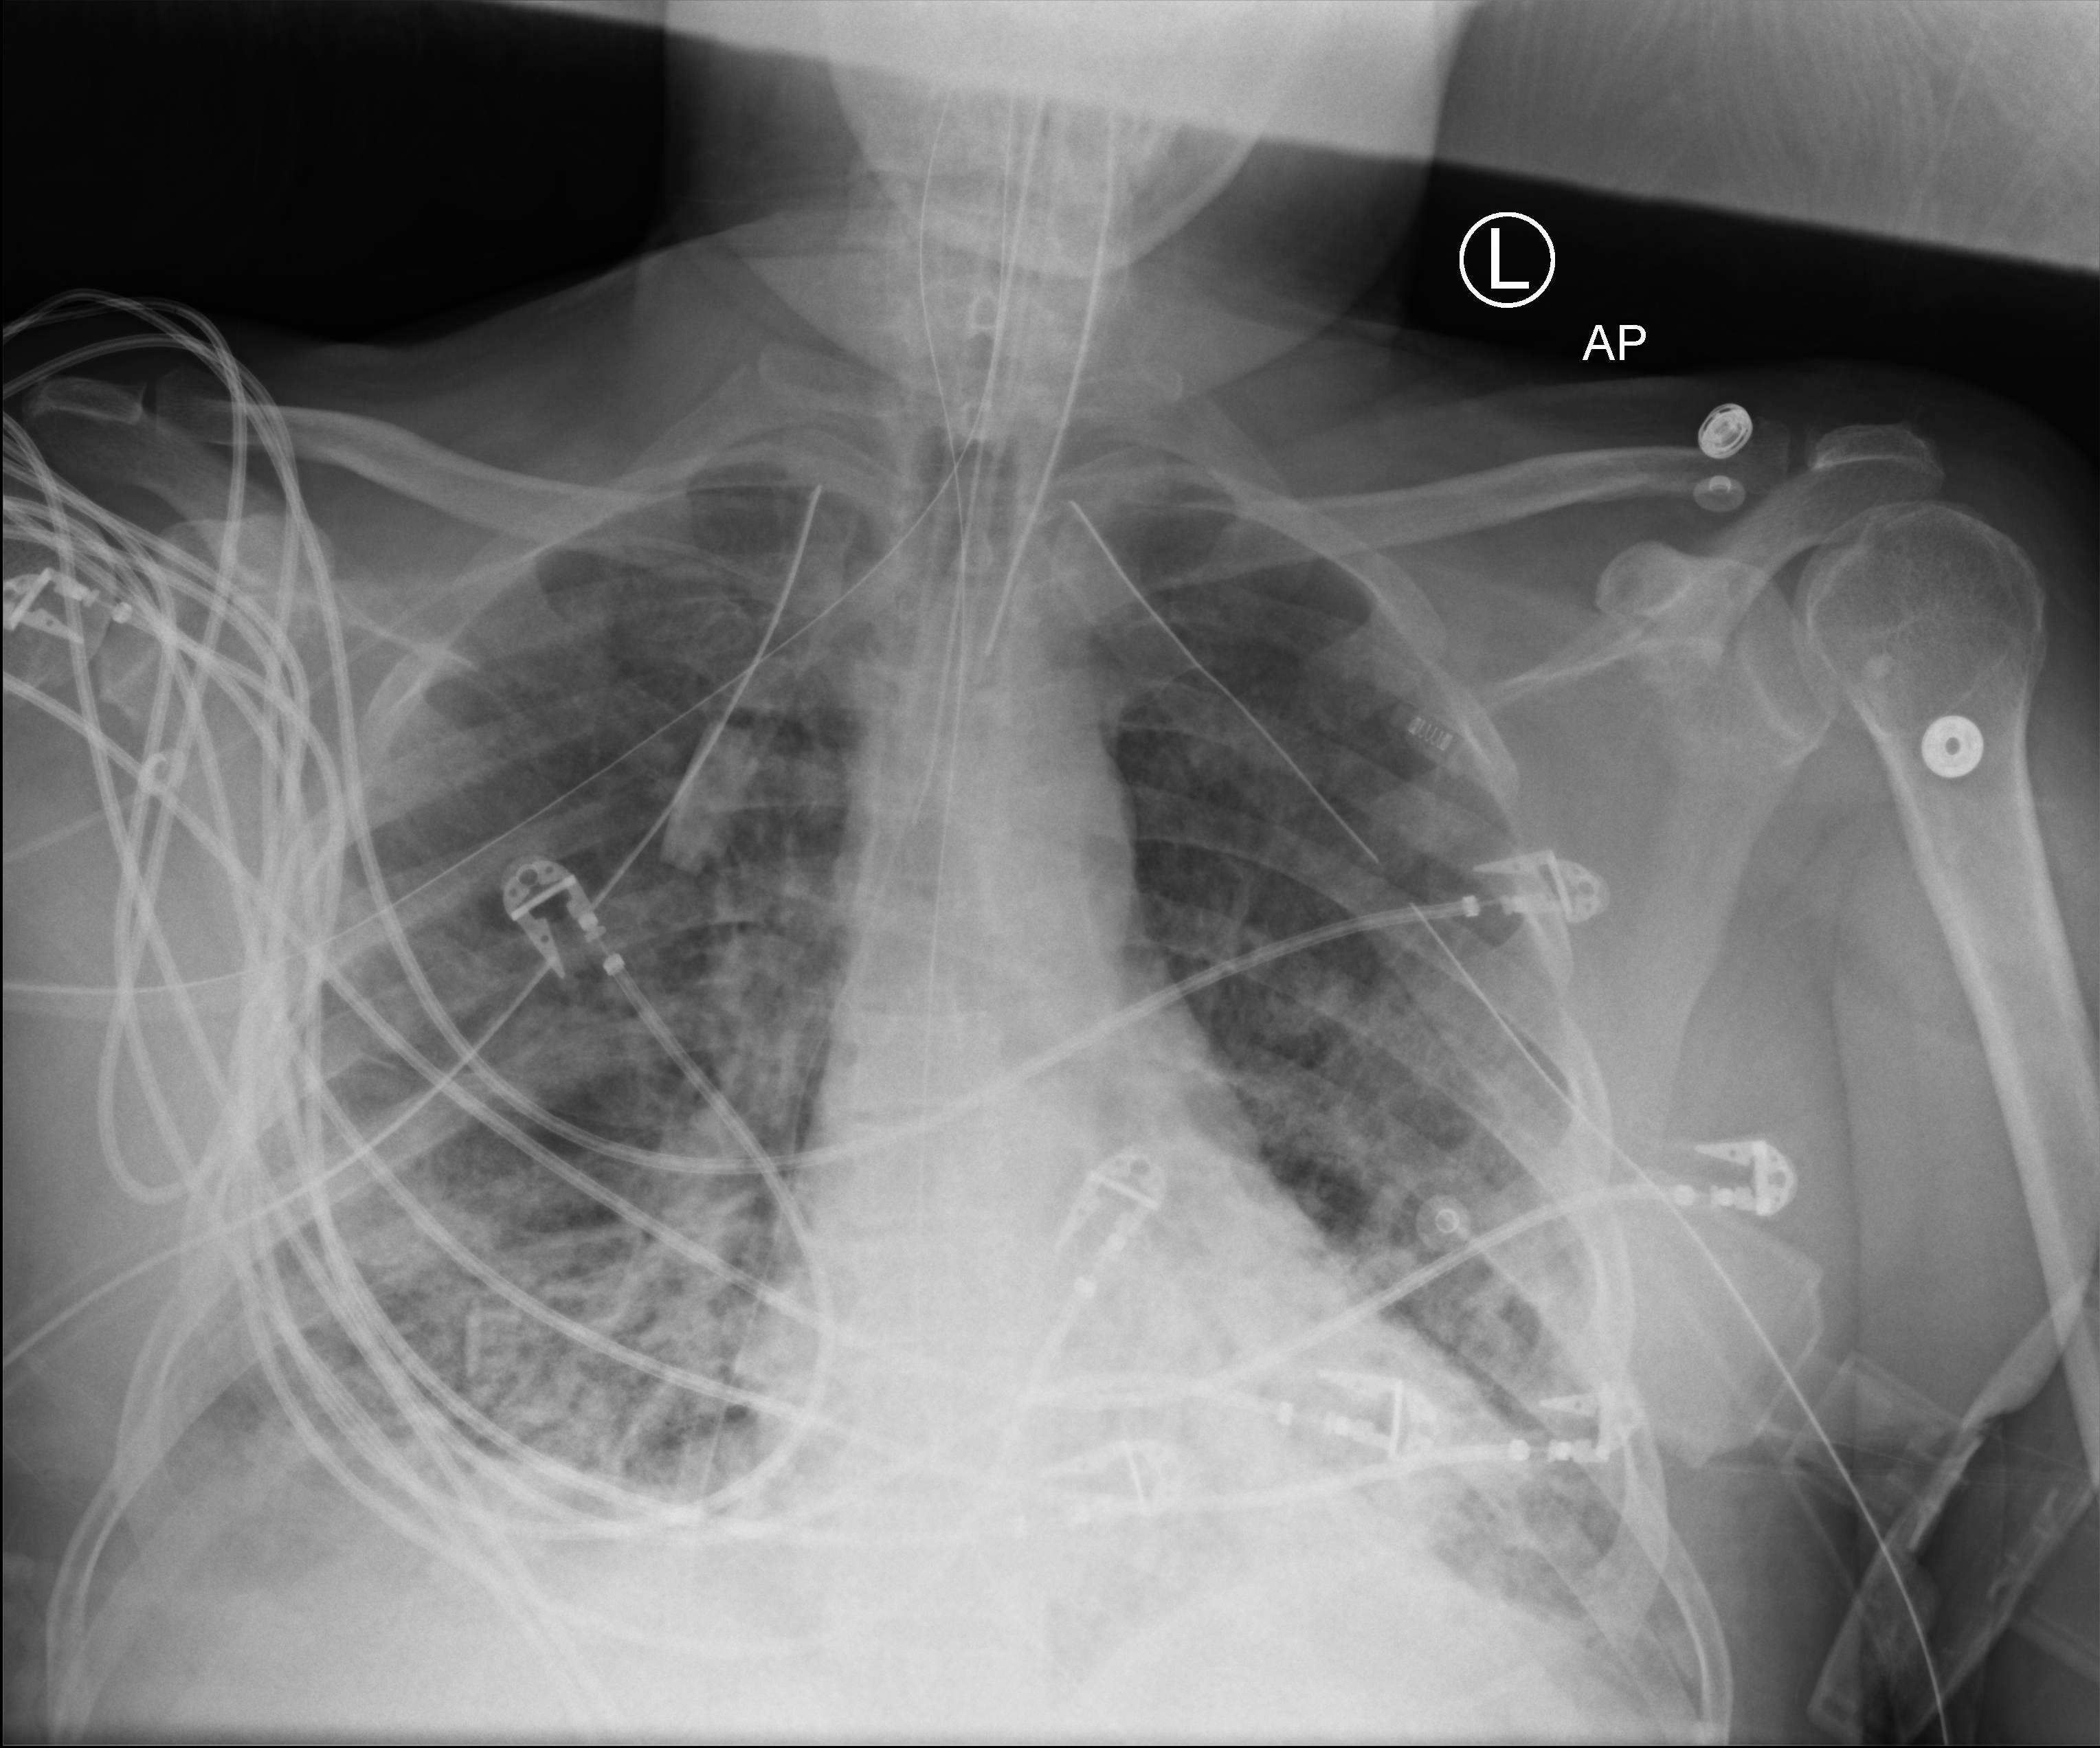
Chest X-ray (portable), anteroposterior (AP) projection. Patient hospitalised with COVID-19; male, aged 18–59 years.
Hospital-stay facts (about this admission, not read from this image; timing relative to this image not recorded):
- mechanically ventilated during this hospital stay: yes
- admitted to intensive care during this hospital stay: yes